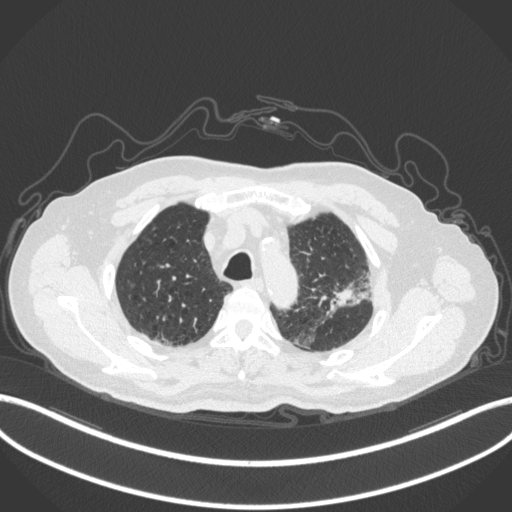
Chest CT, one axial slice. Slice 241 of 331 in the series (ordered by position). 120 kVp. Lung window (W 1500 / L -600 HU). 512 × 512 image matrix, field of view 400 × 400 mm. Patient: male, 79 years. From the clinical record (not read from this slice): clinical TNM (as recorded): T2a N1 M1; histopathological grade: G3.
Outlined on this slice (rectangle marked by the reading radiologist):
- lung tumour (recorded histology: adenocarcinoma): bounding box (x1, y1, x2, y2) in pixels: (316, 271, 373, 322)